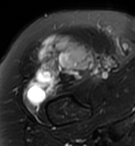
MRI of an extremity soft-tissue mass, one axial slice. Slice 75 of 95 in the series (ordered by position). T2-weighted fat-saturated. MR volume resampled by the dataset authors to the PET/CT grid (not the native acquisition matrix). 3.27 mm slice thickness. 135 × 146 image matrix, field of view 132 × 143 mm. Female patient. Case-level facts recorded for this patient, not image findings: histological type: pleiomorphic undifferentiated sarcoma; grade: high; site of the primary tumour: right quadricep.
Structures marked on this image (expert contour drawn on MRI and transferred to this co-registered scan by the dataset authors):
- gross tumour volume including surrounding oedema: box from (x=25, y=34) to (x=95, y=106) px
- gross tumour volume (mass): (x=25, y=34)–(x=95, y=106)